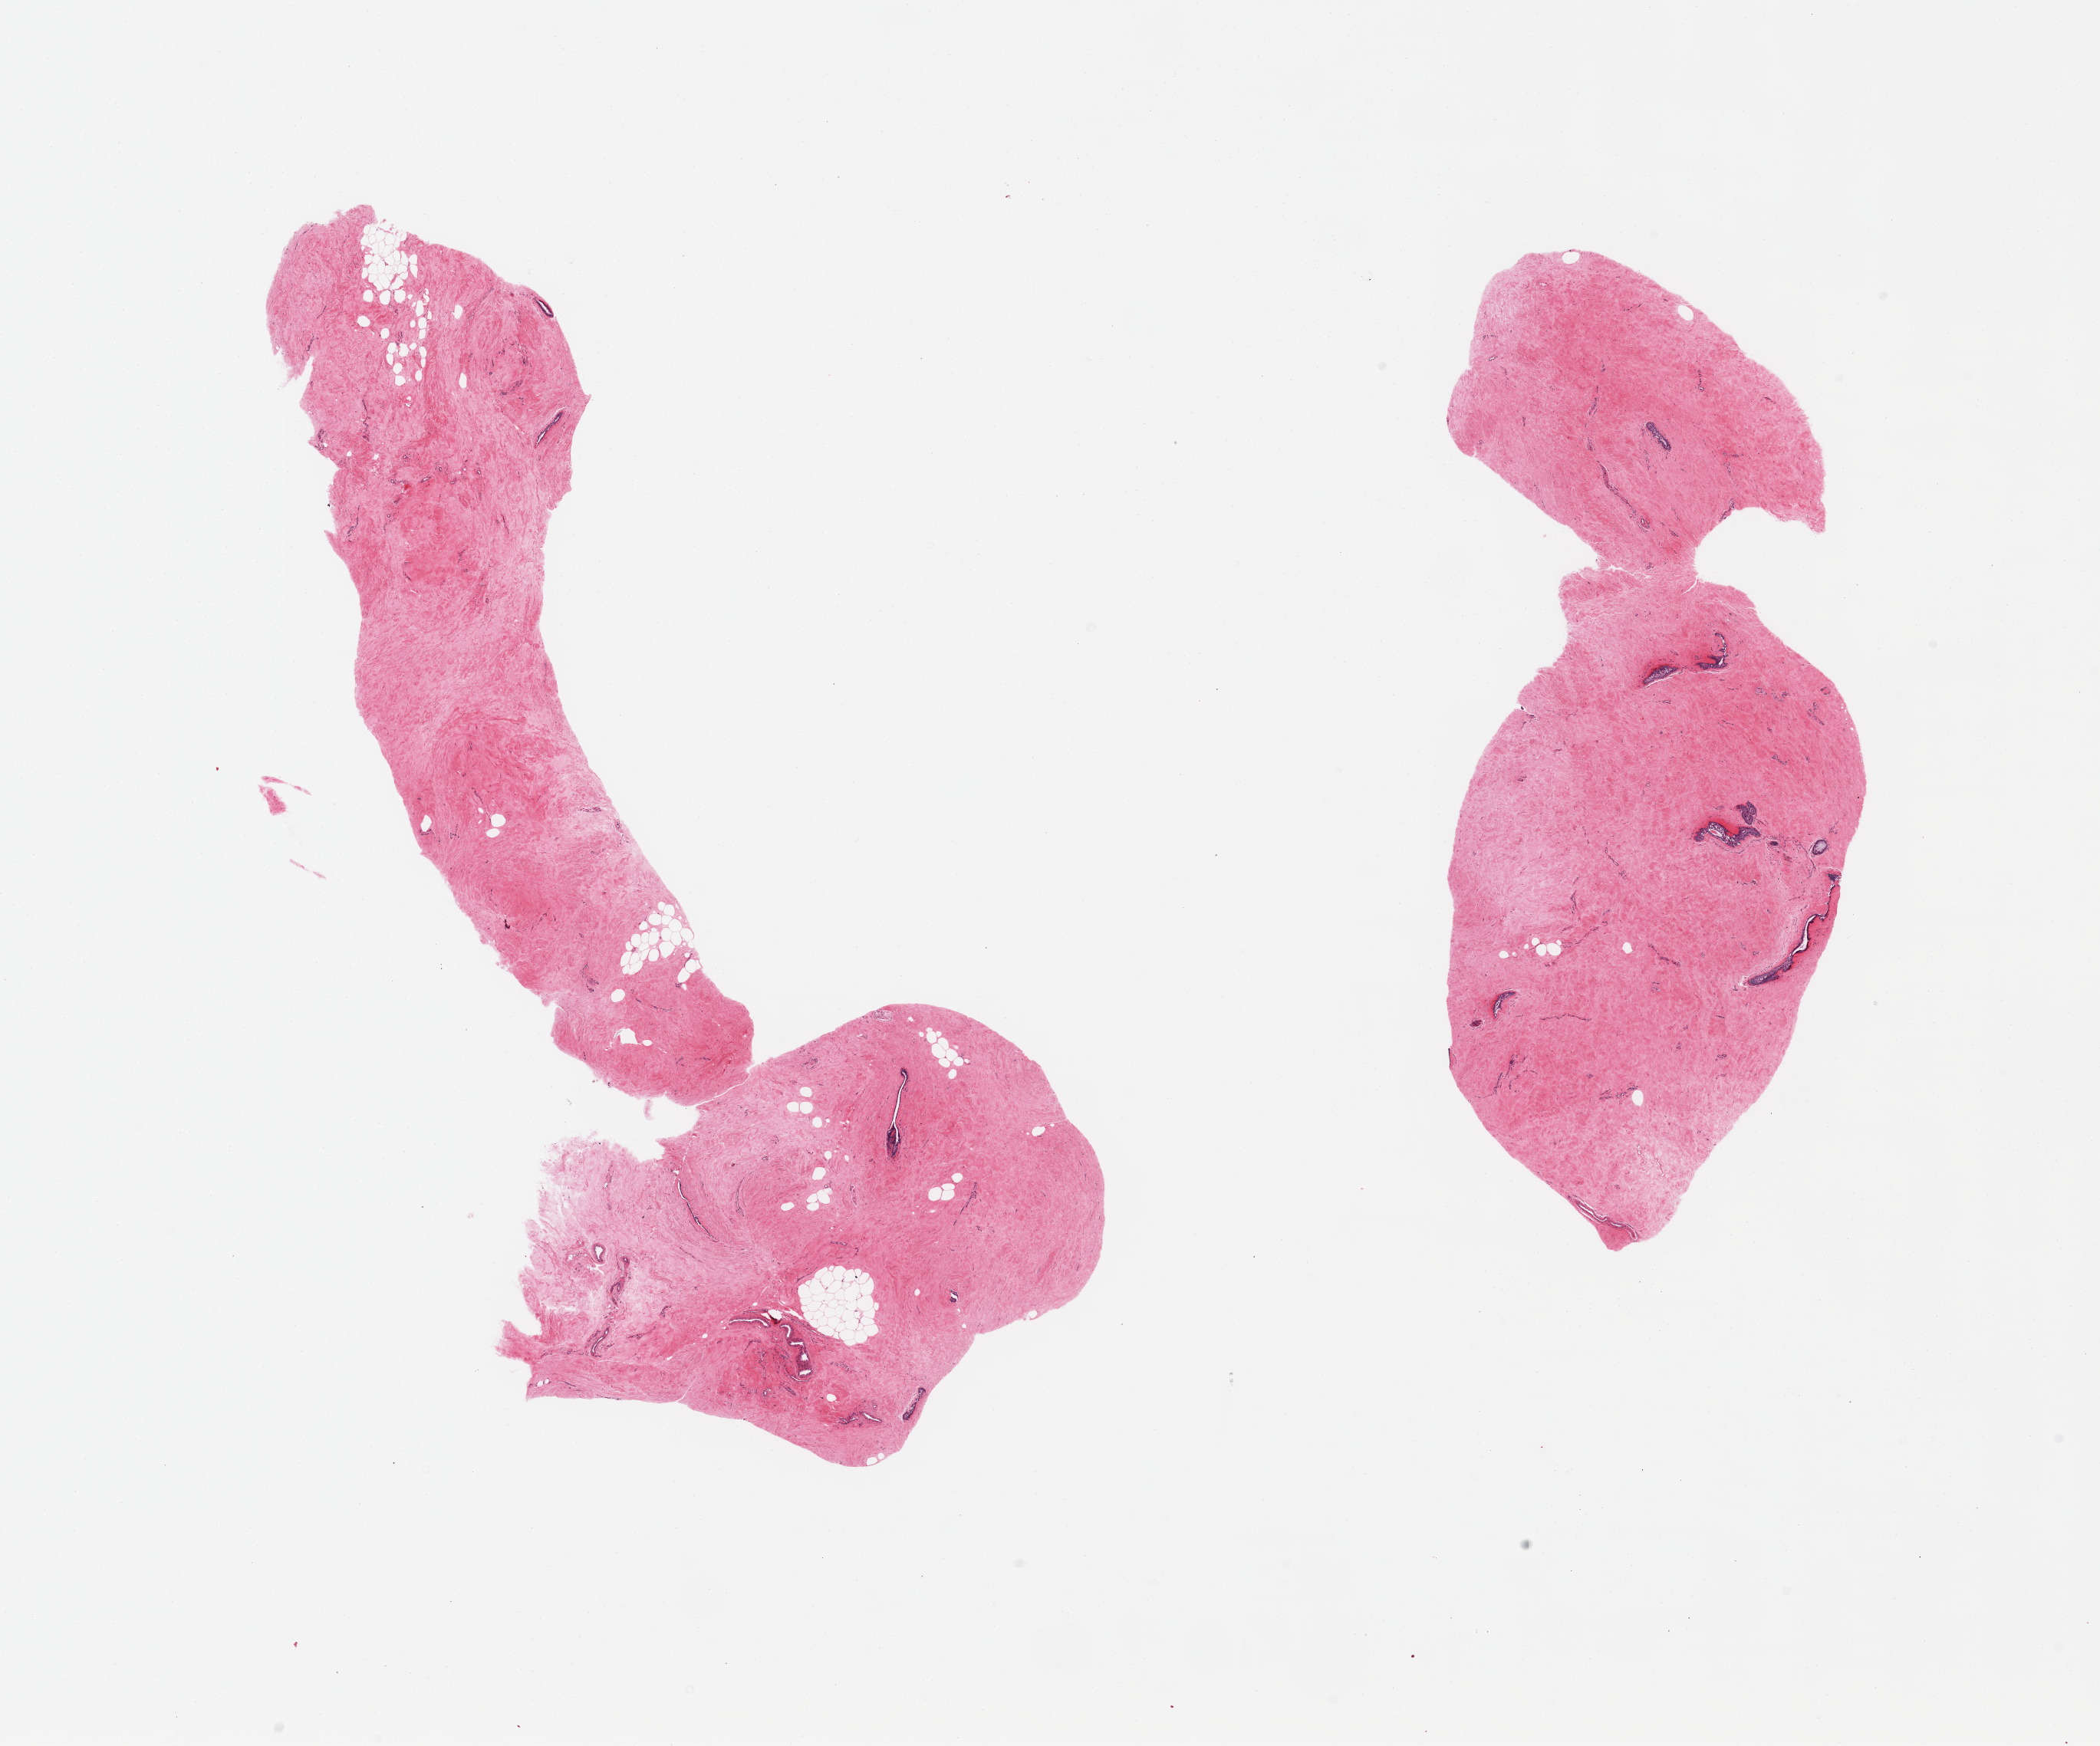
Whole-slide image, haematoxylin and eosin stain — shown as a low-resolution overview of the whole scanned area (about 21.7 x 18.0 mm); PAXgene-fixed, paraffin-embedded tissue; target tissue: breast; tissue donor sample. Donor: male.
• pathologist's review note for this sample: 2 pieces, gynecomastoid stromal and duct (re) hyperplasia